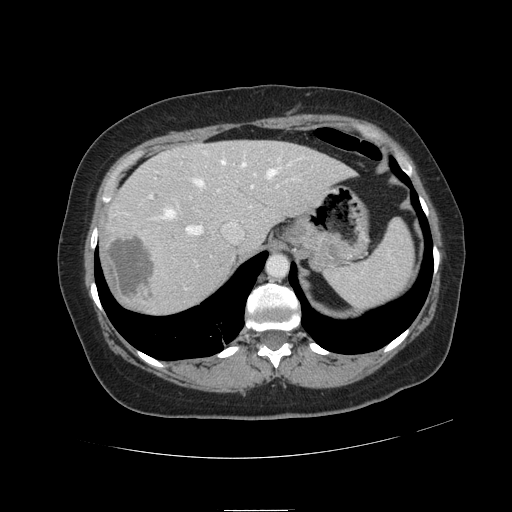
Contrast-enhanced abdominal CT, one axial slice. Slice 89 of 121 in the series (ordered by position). 120 kVp. Soft-tissue window (W 400 / L 40 HU). 512 × 512 image matrix, field of view 400 × 400 mm. Female patient, age 52 years. From the clinical record (not read from this slice): diagnosis: colorectal cancer liver metastases, imaged before liver resection; multiple liver metastases: yes; largest metastasis: 6.3 cm; chemotherapy before resection: yes.
Outlined on this slice (expert manual segmentation):
- hepatic veins: box from (x=165, y=152) to (x=291, y=235) px
- liver: (x=105, y=141)–(x=351, y=313)
- planned liver remnant (the part of the liver to remain after resection): (x=168, y=141)–(x=352, y=249)
- portal vein (with intrahepatic branches): (x=149, y=178)–(x=279, y=290)
- liver metastasis: (x=106, y=234)–(x=155, y=299)